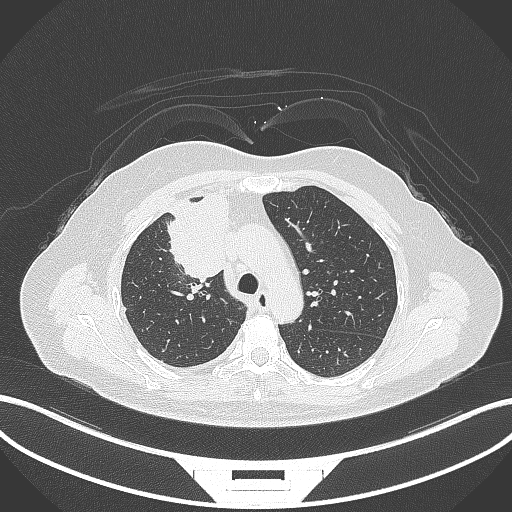
Chest CT, one axial slice. Slice 207 of 305 in the series (ordered by position). 120 kVp. Lung window (W 1500 / L -600 HU). 1 mm slice thickness. 512 × 512 image matrix. Patient: female, 52 years. Case-level facts recorded for this patient, not image findings: clinical TNM (as recorded): T3 N1 M1.
Outlined on this slice (rectangle marked by the reading radiologist):
- lung tumour (recorded histology: adenocarcinoma): bounding box [x1, y1, x2, y2] px = [163, 190, 233, 281]